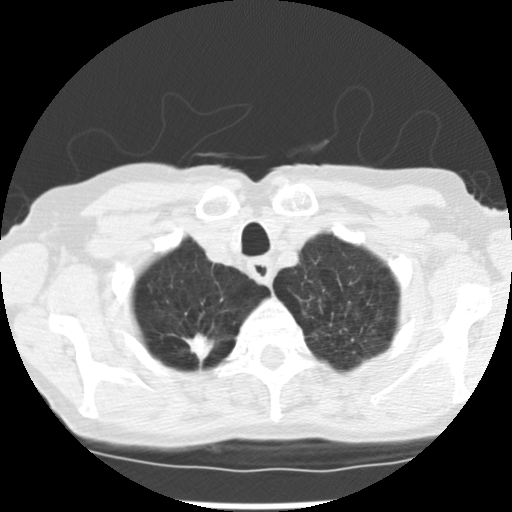
Low-dose screening chest CT, axial slice. Baseline annual screen. Lung window (W 1500 / L -600 HU). 2.5 mm slice thickness. Female, age 72 years at enrolment.
Expert-annotated lung lesion, bounding box [x1, y1, x2, y2] px = [170, 316, 231, 361]. The screening reader recorded 3 non-calcified nodules or masses ≥4 mm on this exam (right upper lobe, left upper lobe, left lower lobe); which of them this box marks is not recorded. Official screen result: positive, change unspecified: nodule(s) >= 4 mm or enlarging nodule(s), mass(es), or other non-specific abnormalities suspicious for lung cancer.